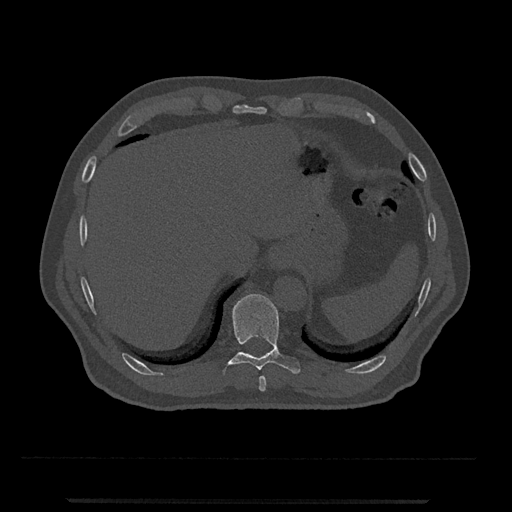
CT including the spine, one axial slice. Slice 519 of 797 in the series (ordered by position). Reconstruction kernel Br40s/3. 120 kVp. Bone window (W 1800 / L 400 HU). 0.5 mm slice thickness. 512 × 512 image matrix, field of view 419 × 419 mm. Male patient, age 63 years. From the clinical record (not read from this slice): primary cancer: prostate.
Structures marked on this image (semi-automatic segmentation, software-assisted and operator-edited):
- T10 vertebra: bounding box [x1, y1, x2, y2] px = [222, 294, 301, 374]
- T9 vertebra: [259, 376, 267, 392]